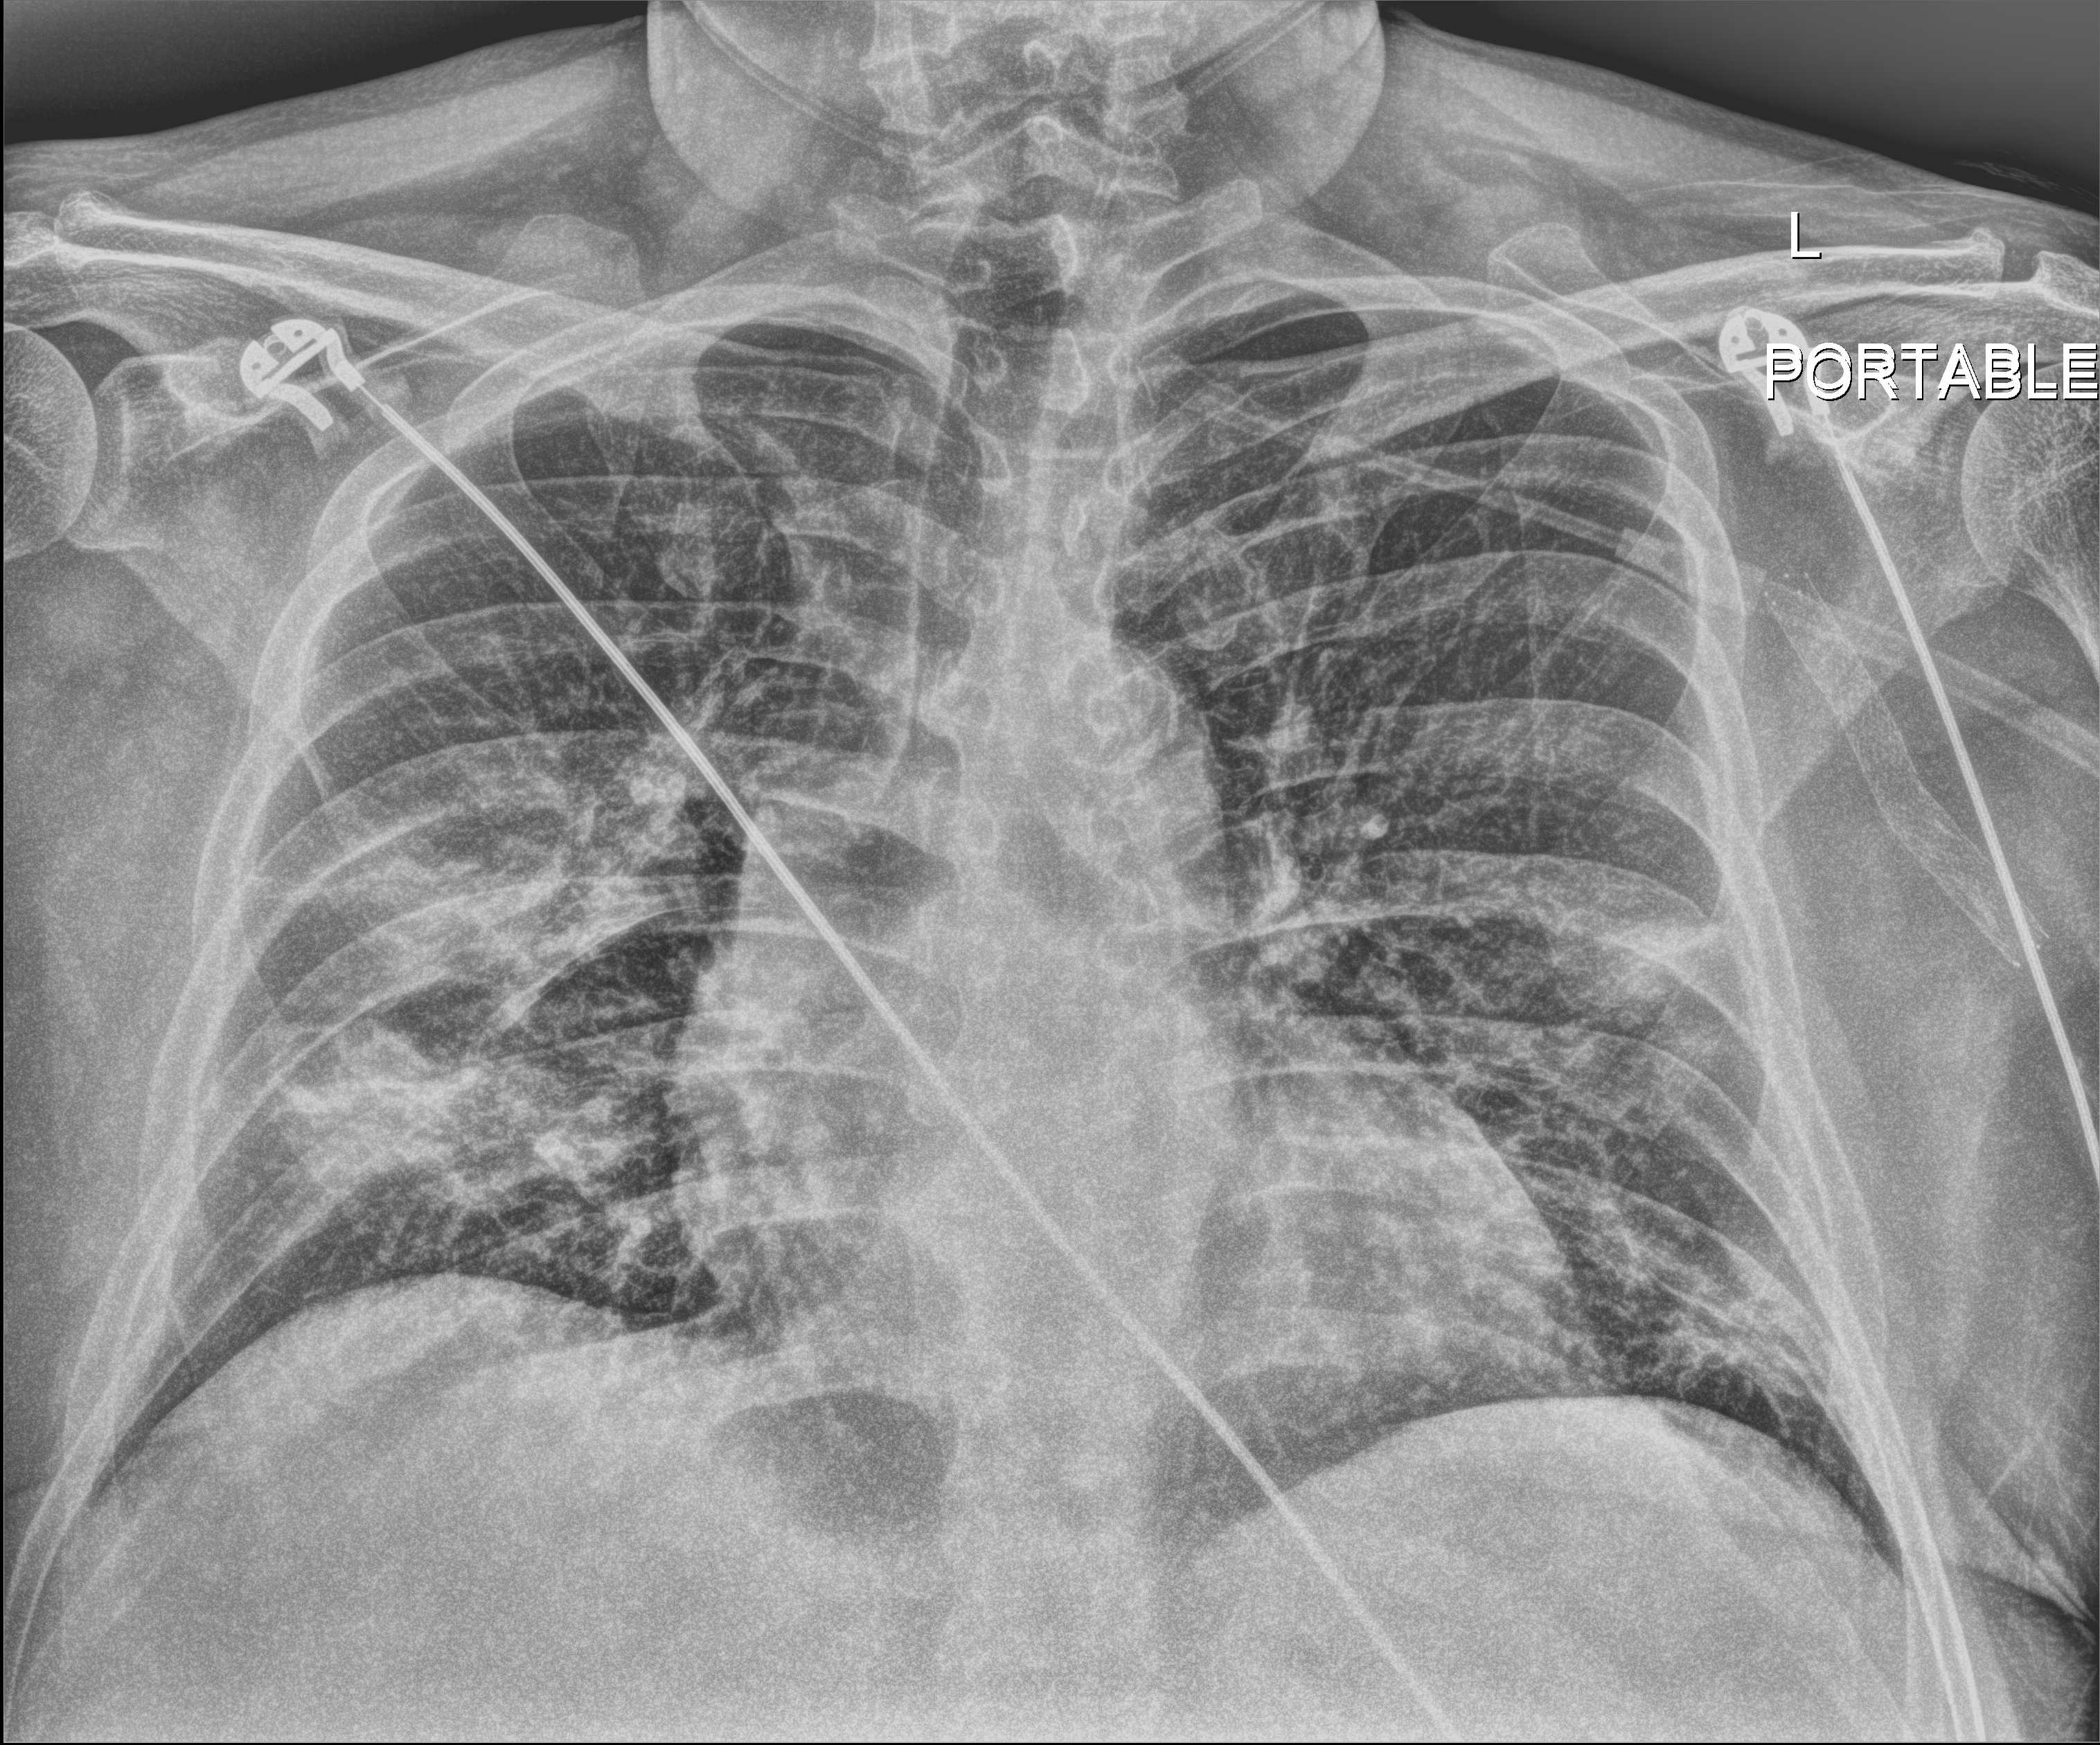
Chest radiograph (digital radiography), anteroposterior (AP) projection. Male patient hospitalised with COVID-19, age 18–59 years.
Admission-level facts for this patient (not findings on this image; timing relative to this image not recorded): admitted to intensive care during this hospital stay: no; mechanically ventilated during this hospital stay: no.